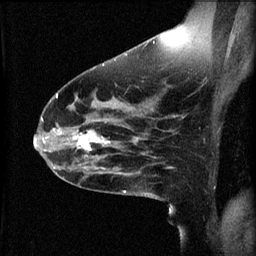
Breast MRI (dynamic contrast-enhanced), one sagittal slice. Position 34 of 60 along the scan axis. 3 images stored at this slice position (order not interpretable as contrast timing). 1.5 T. TE 4.2 ms, TR 8.2 ms. 256 × 256 image matrix, field of view 200 × 200 mm. Patient: female, 49 years.
Structures marked on this image (semi-automatically segmented with operator editing):
- analysis volume of interest (the breast-tissue region the enhancement analysis was run in; not a lesion): bounding box [x1, y1, x2, y2] px = [66, 124, 113, 159]
- tumour enhancement mask (voxels above the 70 % enhancement threshold inside the analysis volume of interest): [74, 130, 111, 153]